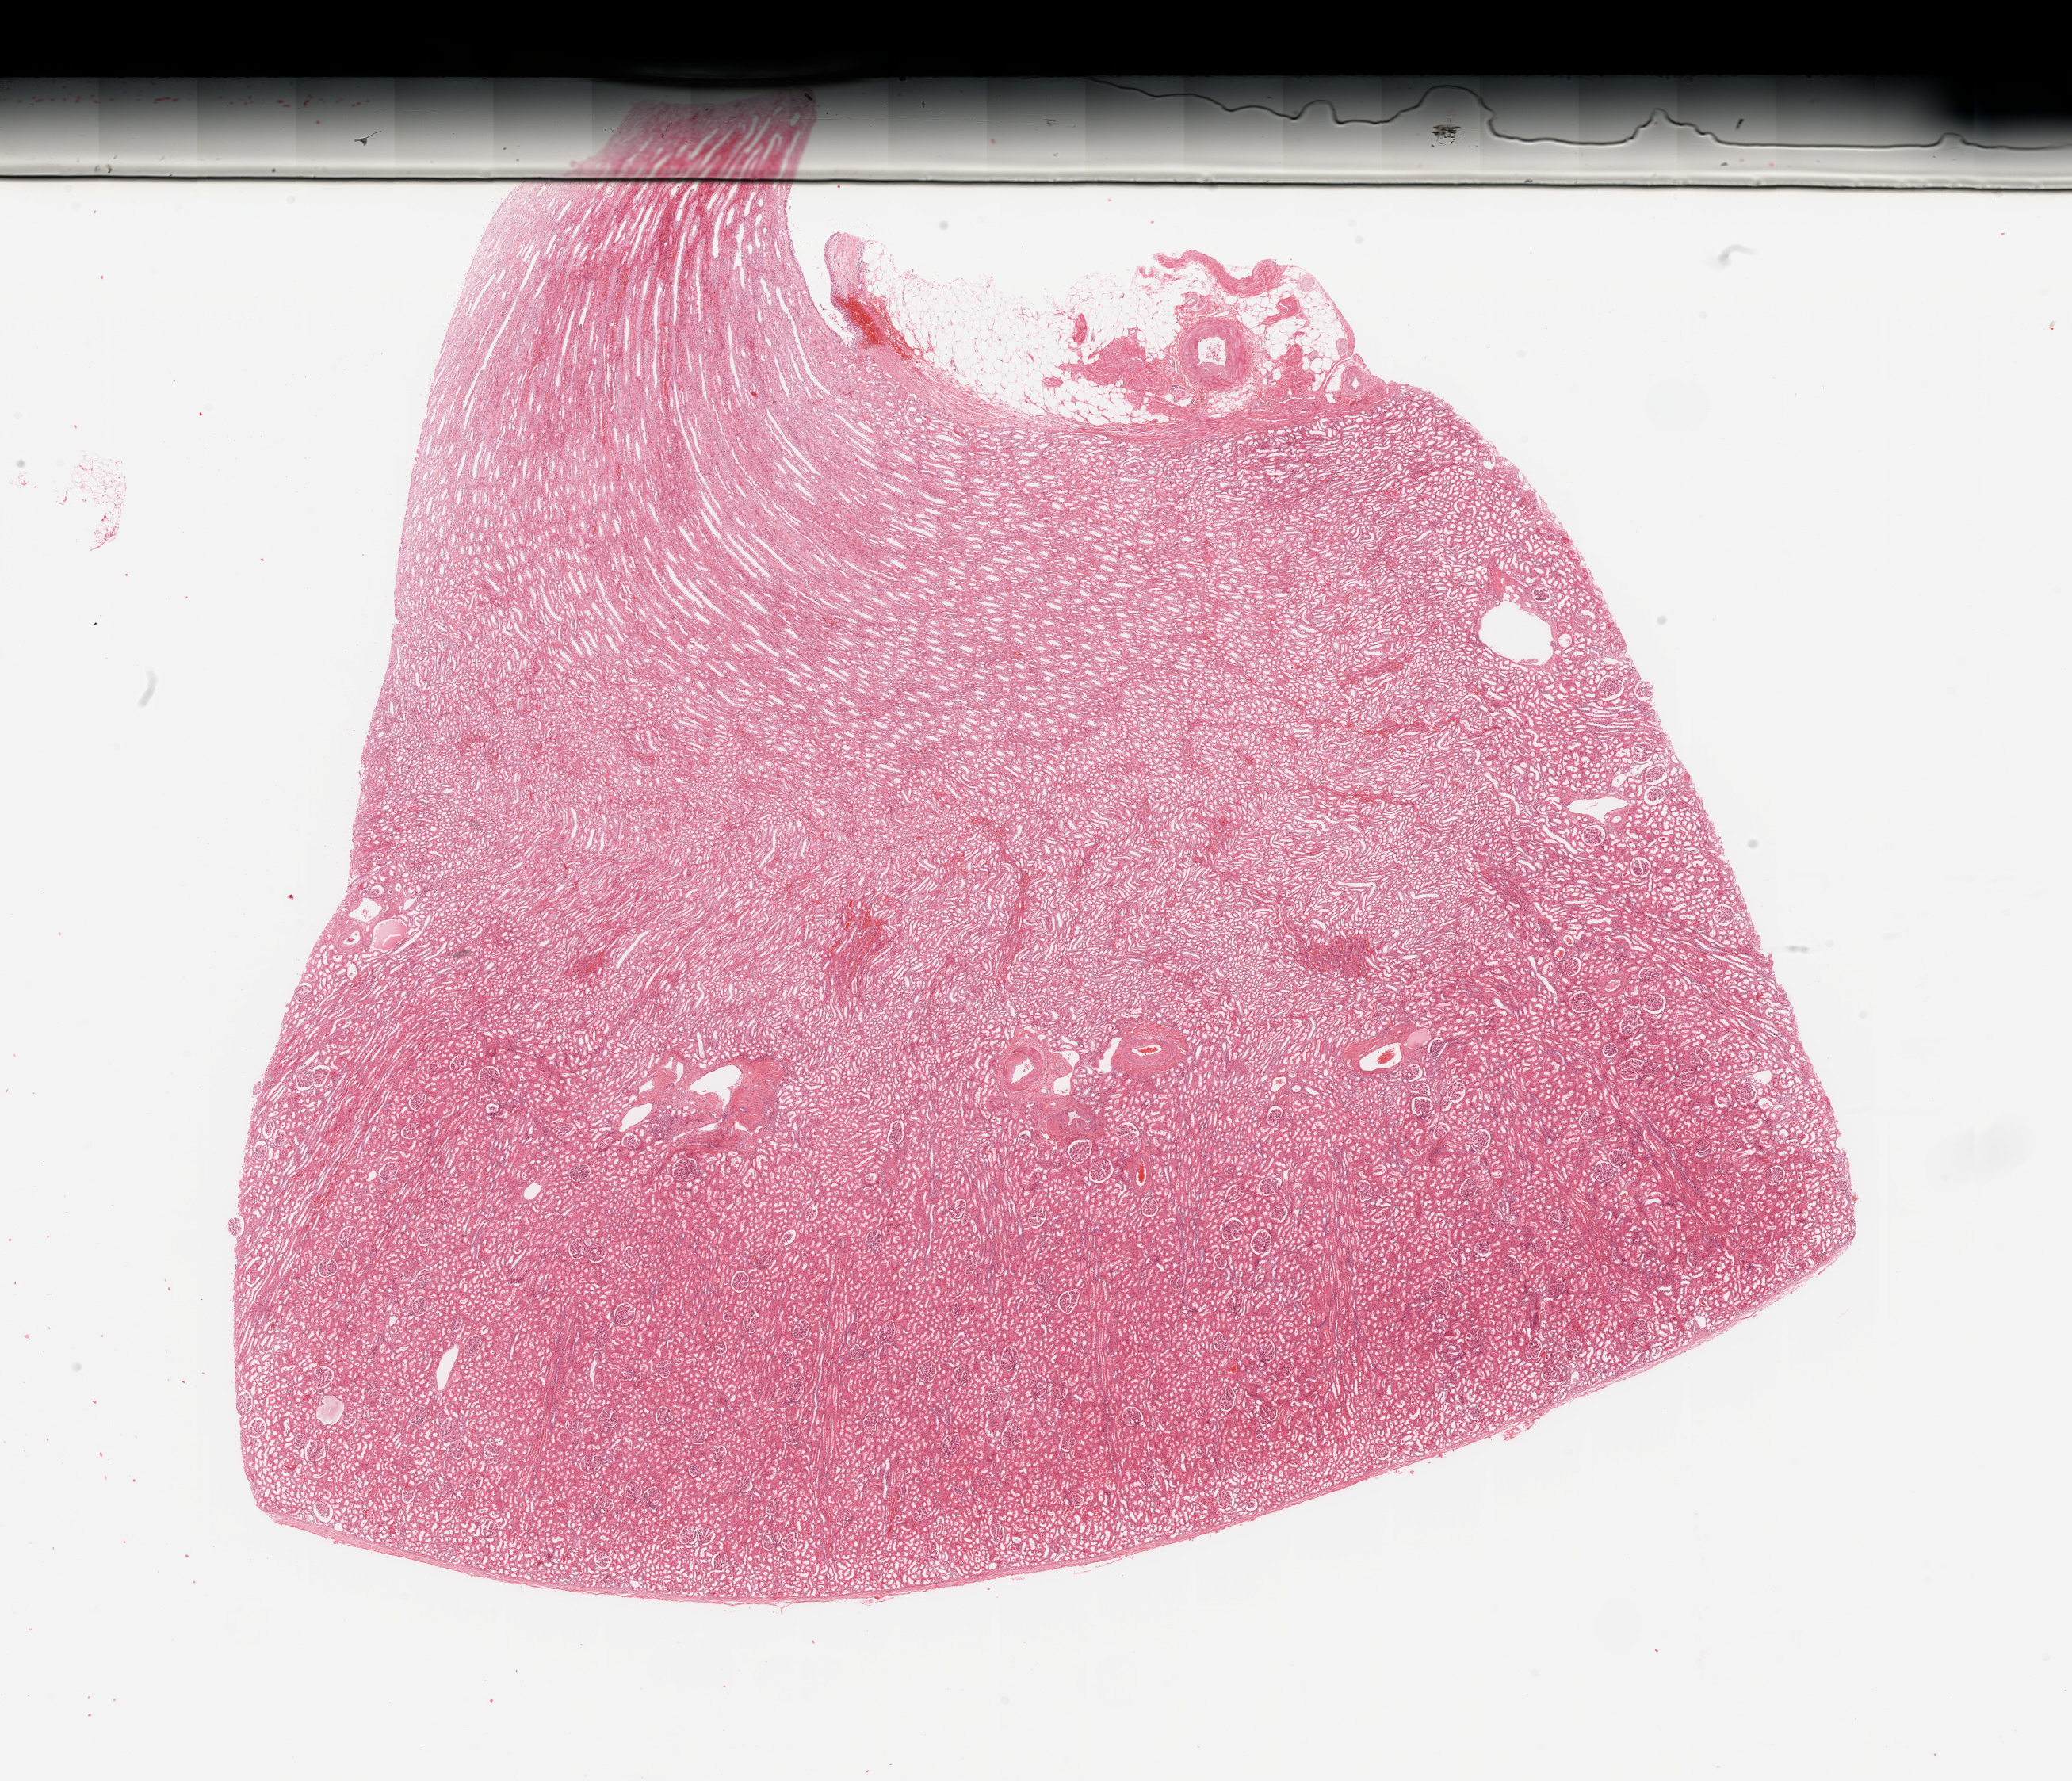
Whole-slide histology image, H&E-stained, whole scanned area (about 20.7 x 17.8 mm, from a 20x scan) shown as a low-resolution overview. Normal (non-tumour) tissue sample, kidney. Patient: male, age 47 years.
• this section: normal (non-tumour) tissue from the same patient
• patient diagnosis: Renal cell carcinoma, NOS